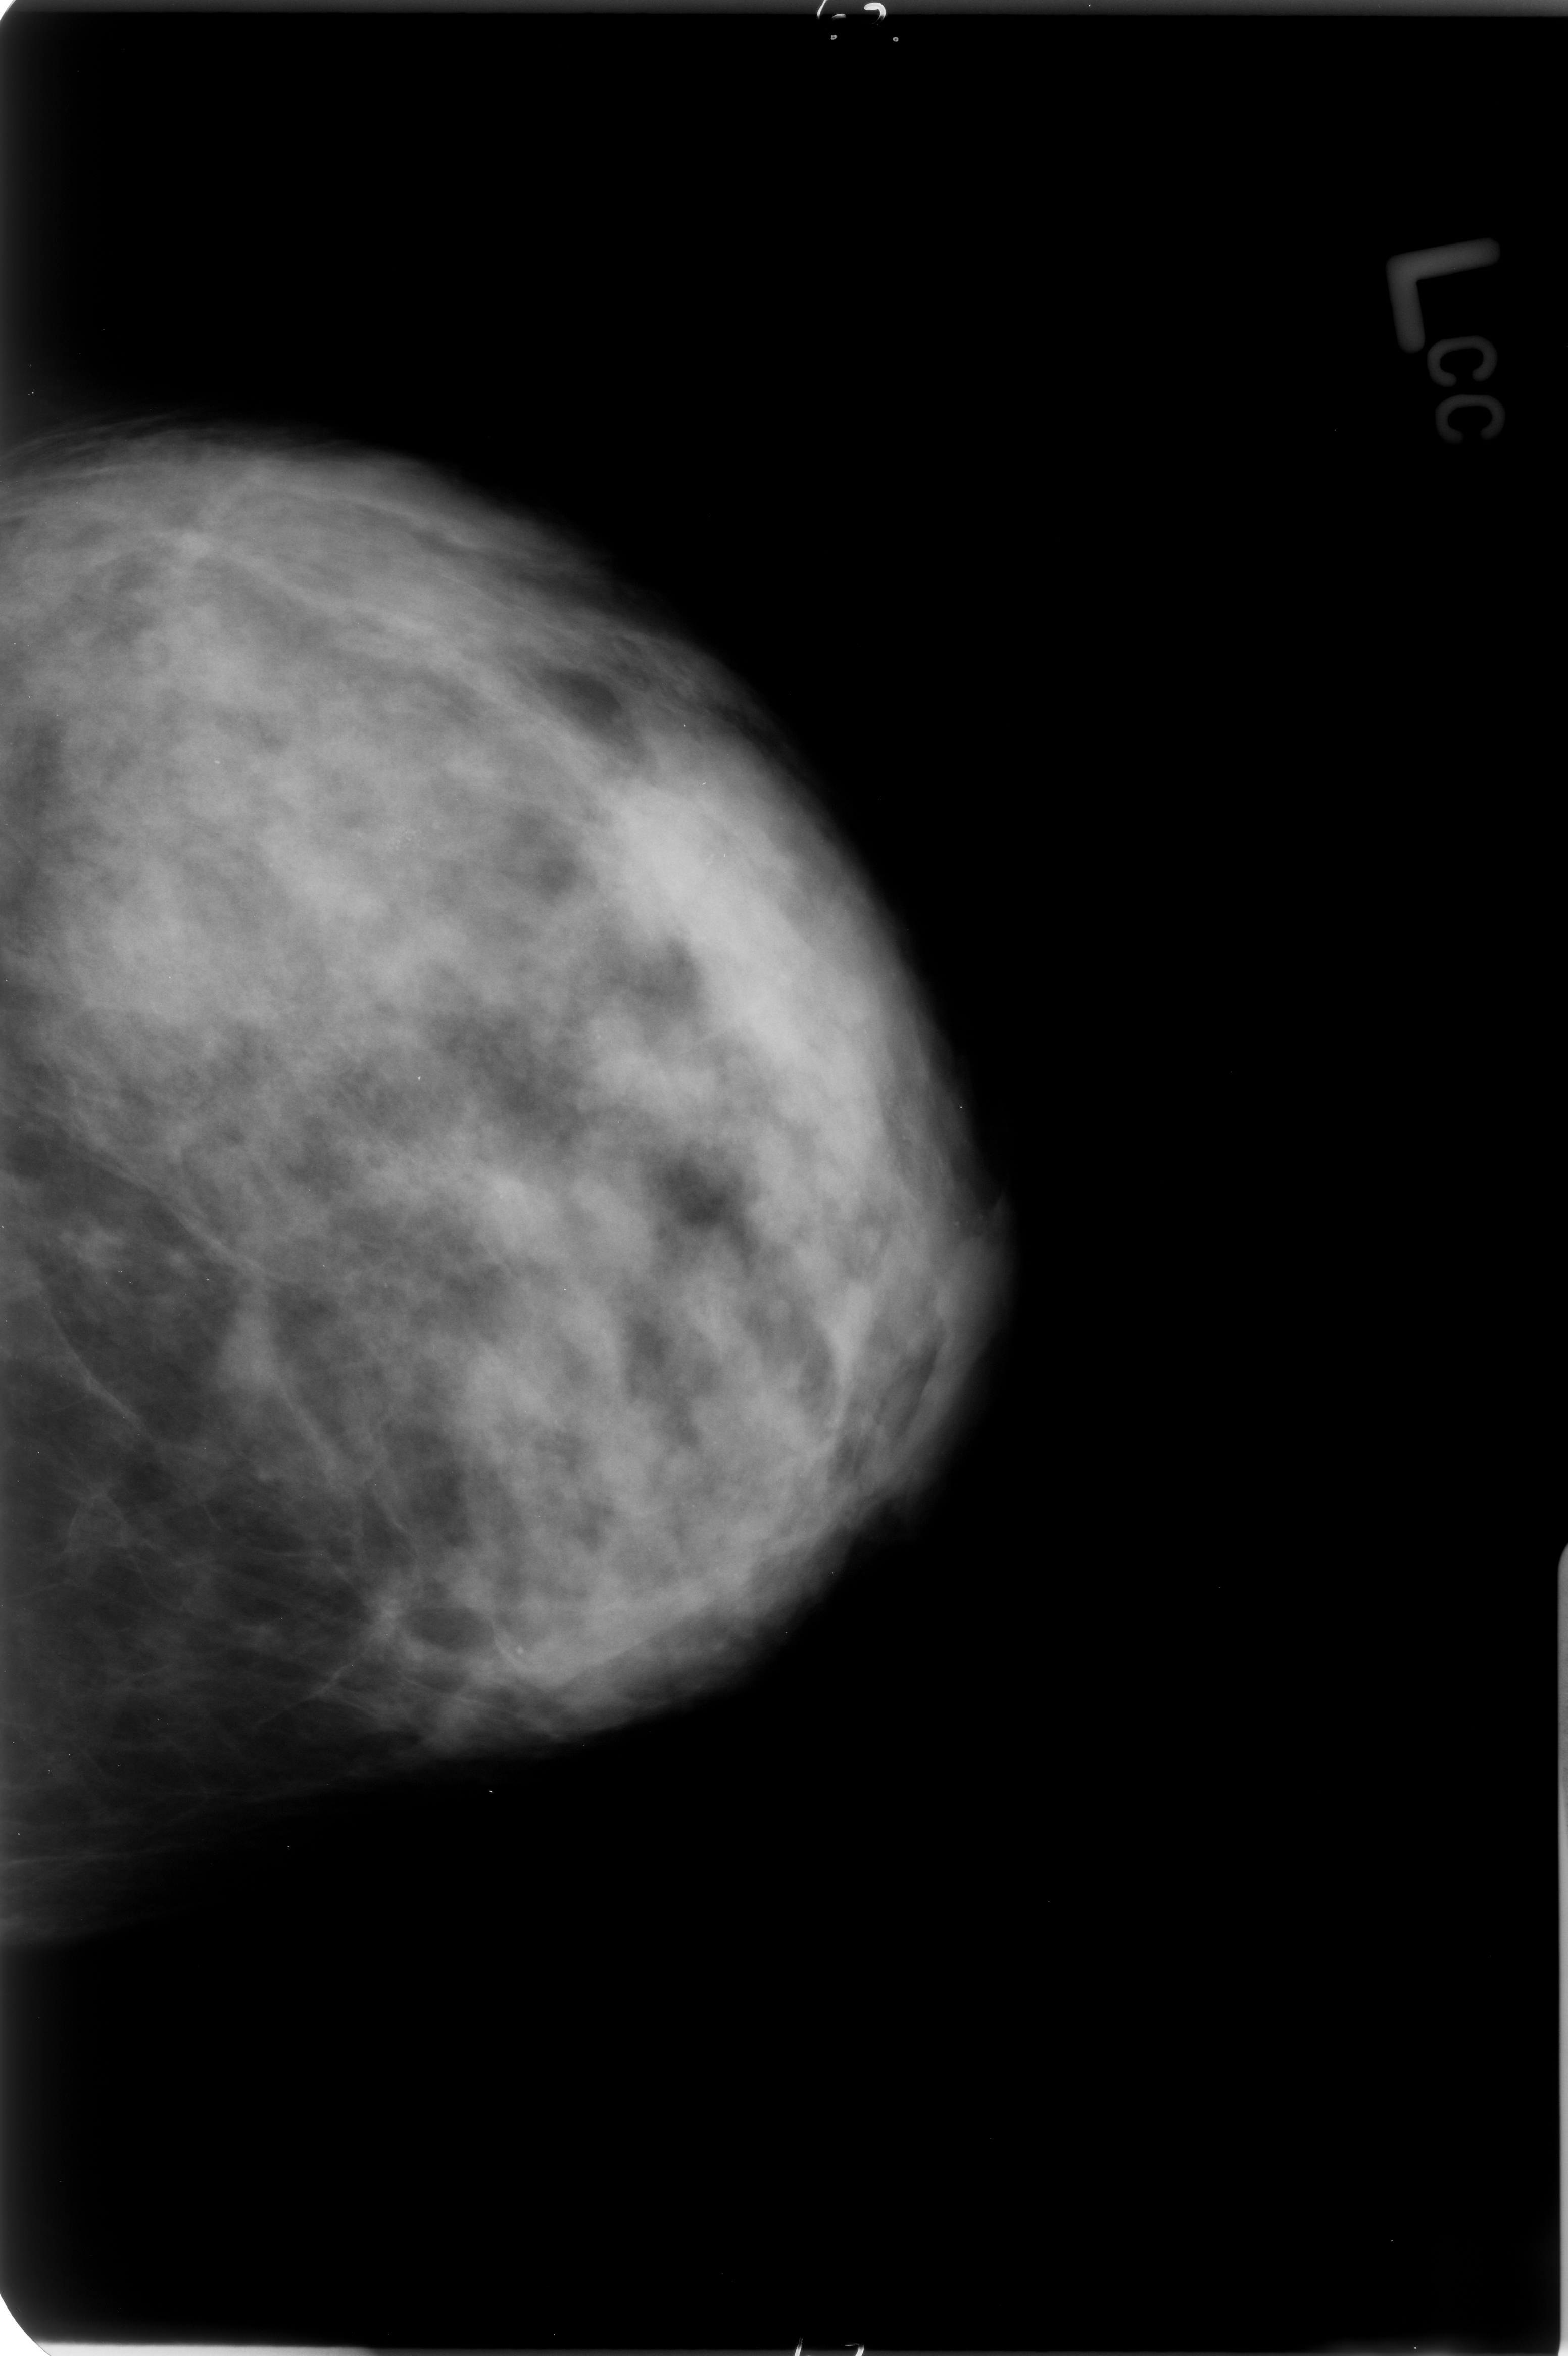
Mammogram (digitized film); left breast; CC view; breast composition: heterogeneously dense (BI-RADS density category 3 of 4).
- Marked findings (only marked abnormalities are described; nothing is implied about the rest of the image): calcifications, morphology pleomorphic, distribution clustered; BI-RADS assessment category 4; pathology result (as recorded, not read from the image): benign.